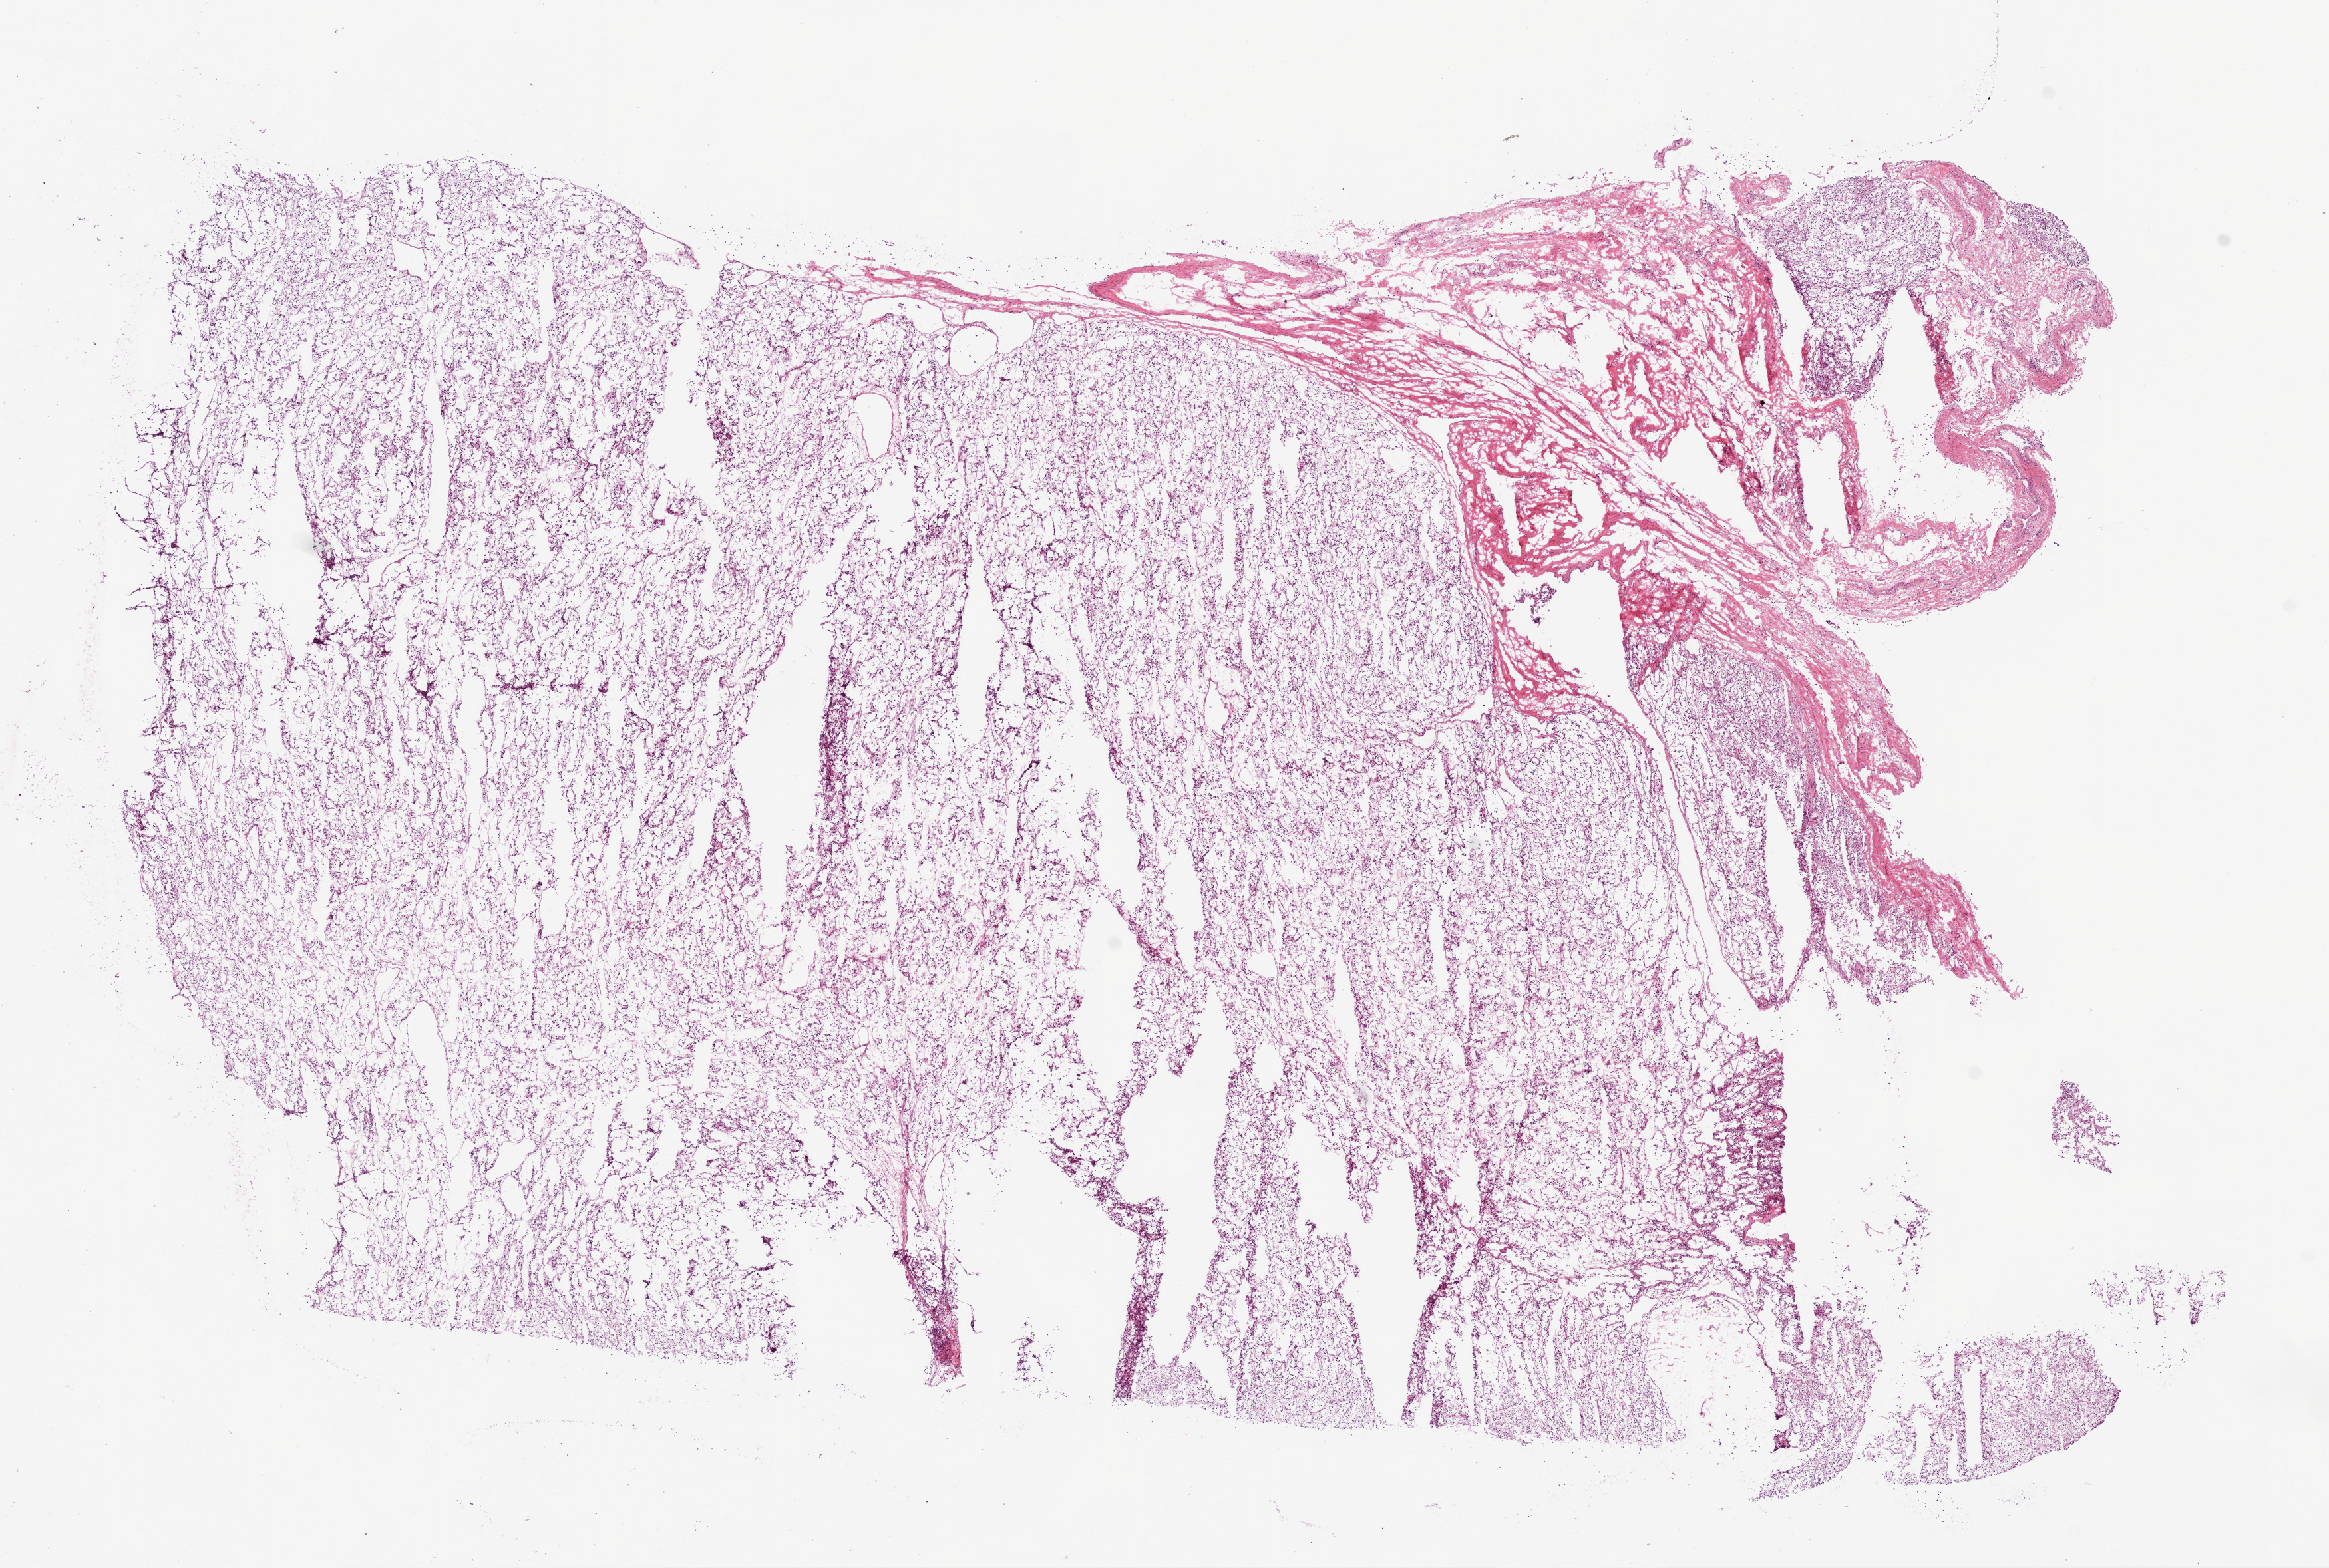
Digitized H&E-stained tissue section (whole slide), shown as a low-resolution overview of the whole scanned area (about 14.0 x 9.5 mm, acquisition: 20x scan); frozen section; kidney, primary tumour sample. Patient: female, age at initial diagnosis 61 years. Histologic grade: G2 (moderately differentiated). Pathologist review of this section (percent, as recorded): tumour cells 85%, tumour nuclei 85%, normal cells 0%, stromal cells 15%, necrosis 0%.
- laterality: right
- AJCC pathologic stage: I
- histologic diagnosis: Clear cell adenocarcinoma, NOS